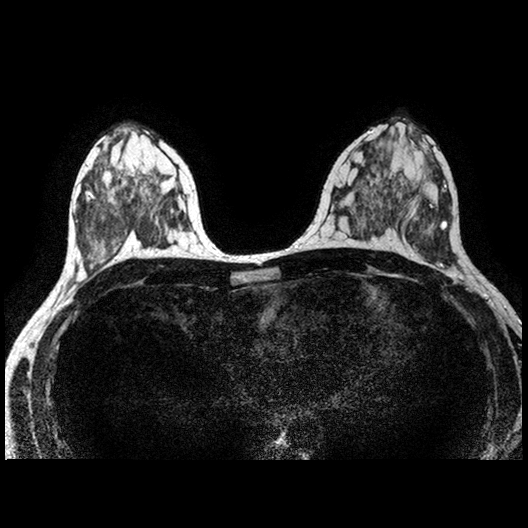
MRI of the breasts; 2 images, each one mid-volume slice chosen by position.
Image 1: fluid-sensitive (T2/STIR) axial slice, slice 43 of 84, 2 mm slice thickness.
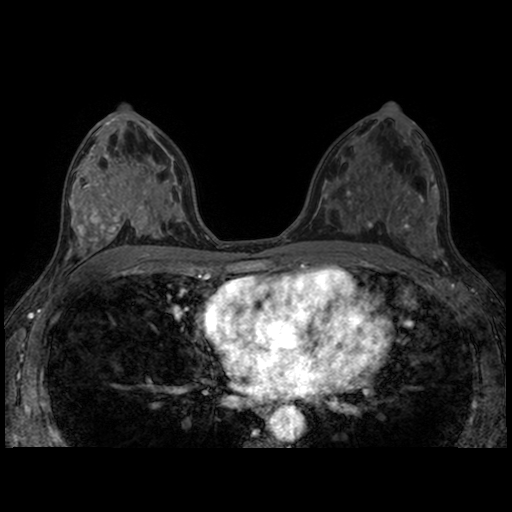
Image 2: post-contrast dynamic axial slice, series "AX BLISS_AUTO SENSE", slice 43 of 84, dynamic phase 5 of 8, 4 mm slice thickness.
Pathology recorded for this patient (not read from these images): pathology diagnosis: benign.